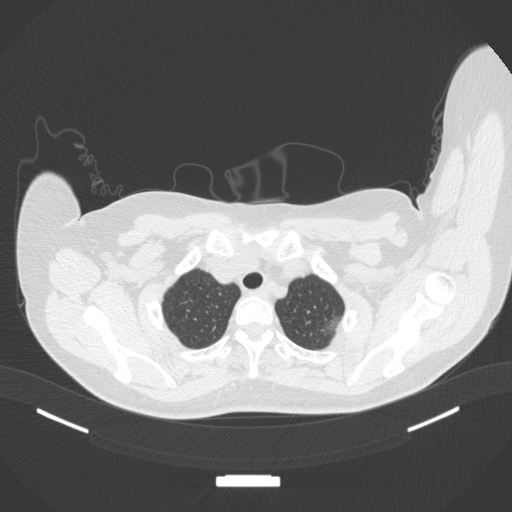
Chest CT, one axial slice; slice 327 of 386 in the series (ordered by position); lung window (W 1500 / L -600 HU); 512 × 512 image matrix, field of view 400 × 400 mm. Female patient, age 58 years. Case-level facts recorded for this patient, not image findings: clinical TNM (as recorded): T1c N0 M0.
Annotated regions visible in this slice (bounding box drawn by a radiologist):
- lung tumour (recorded histology: adenocarcinoma): box from (x=322, y=314) to (x=345, y=339) px